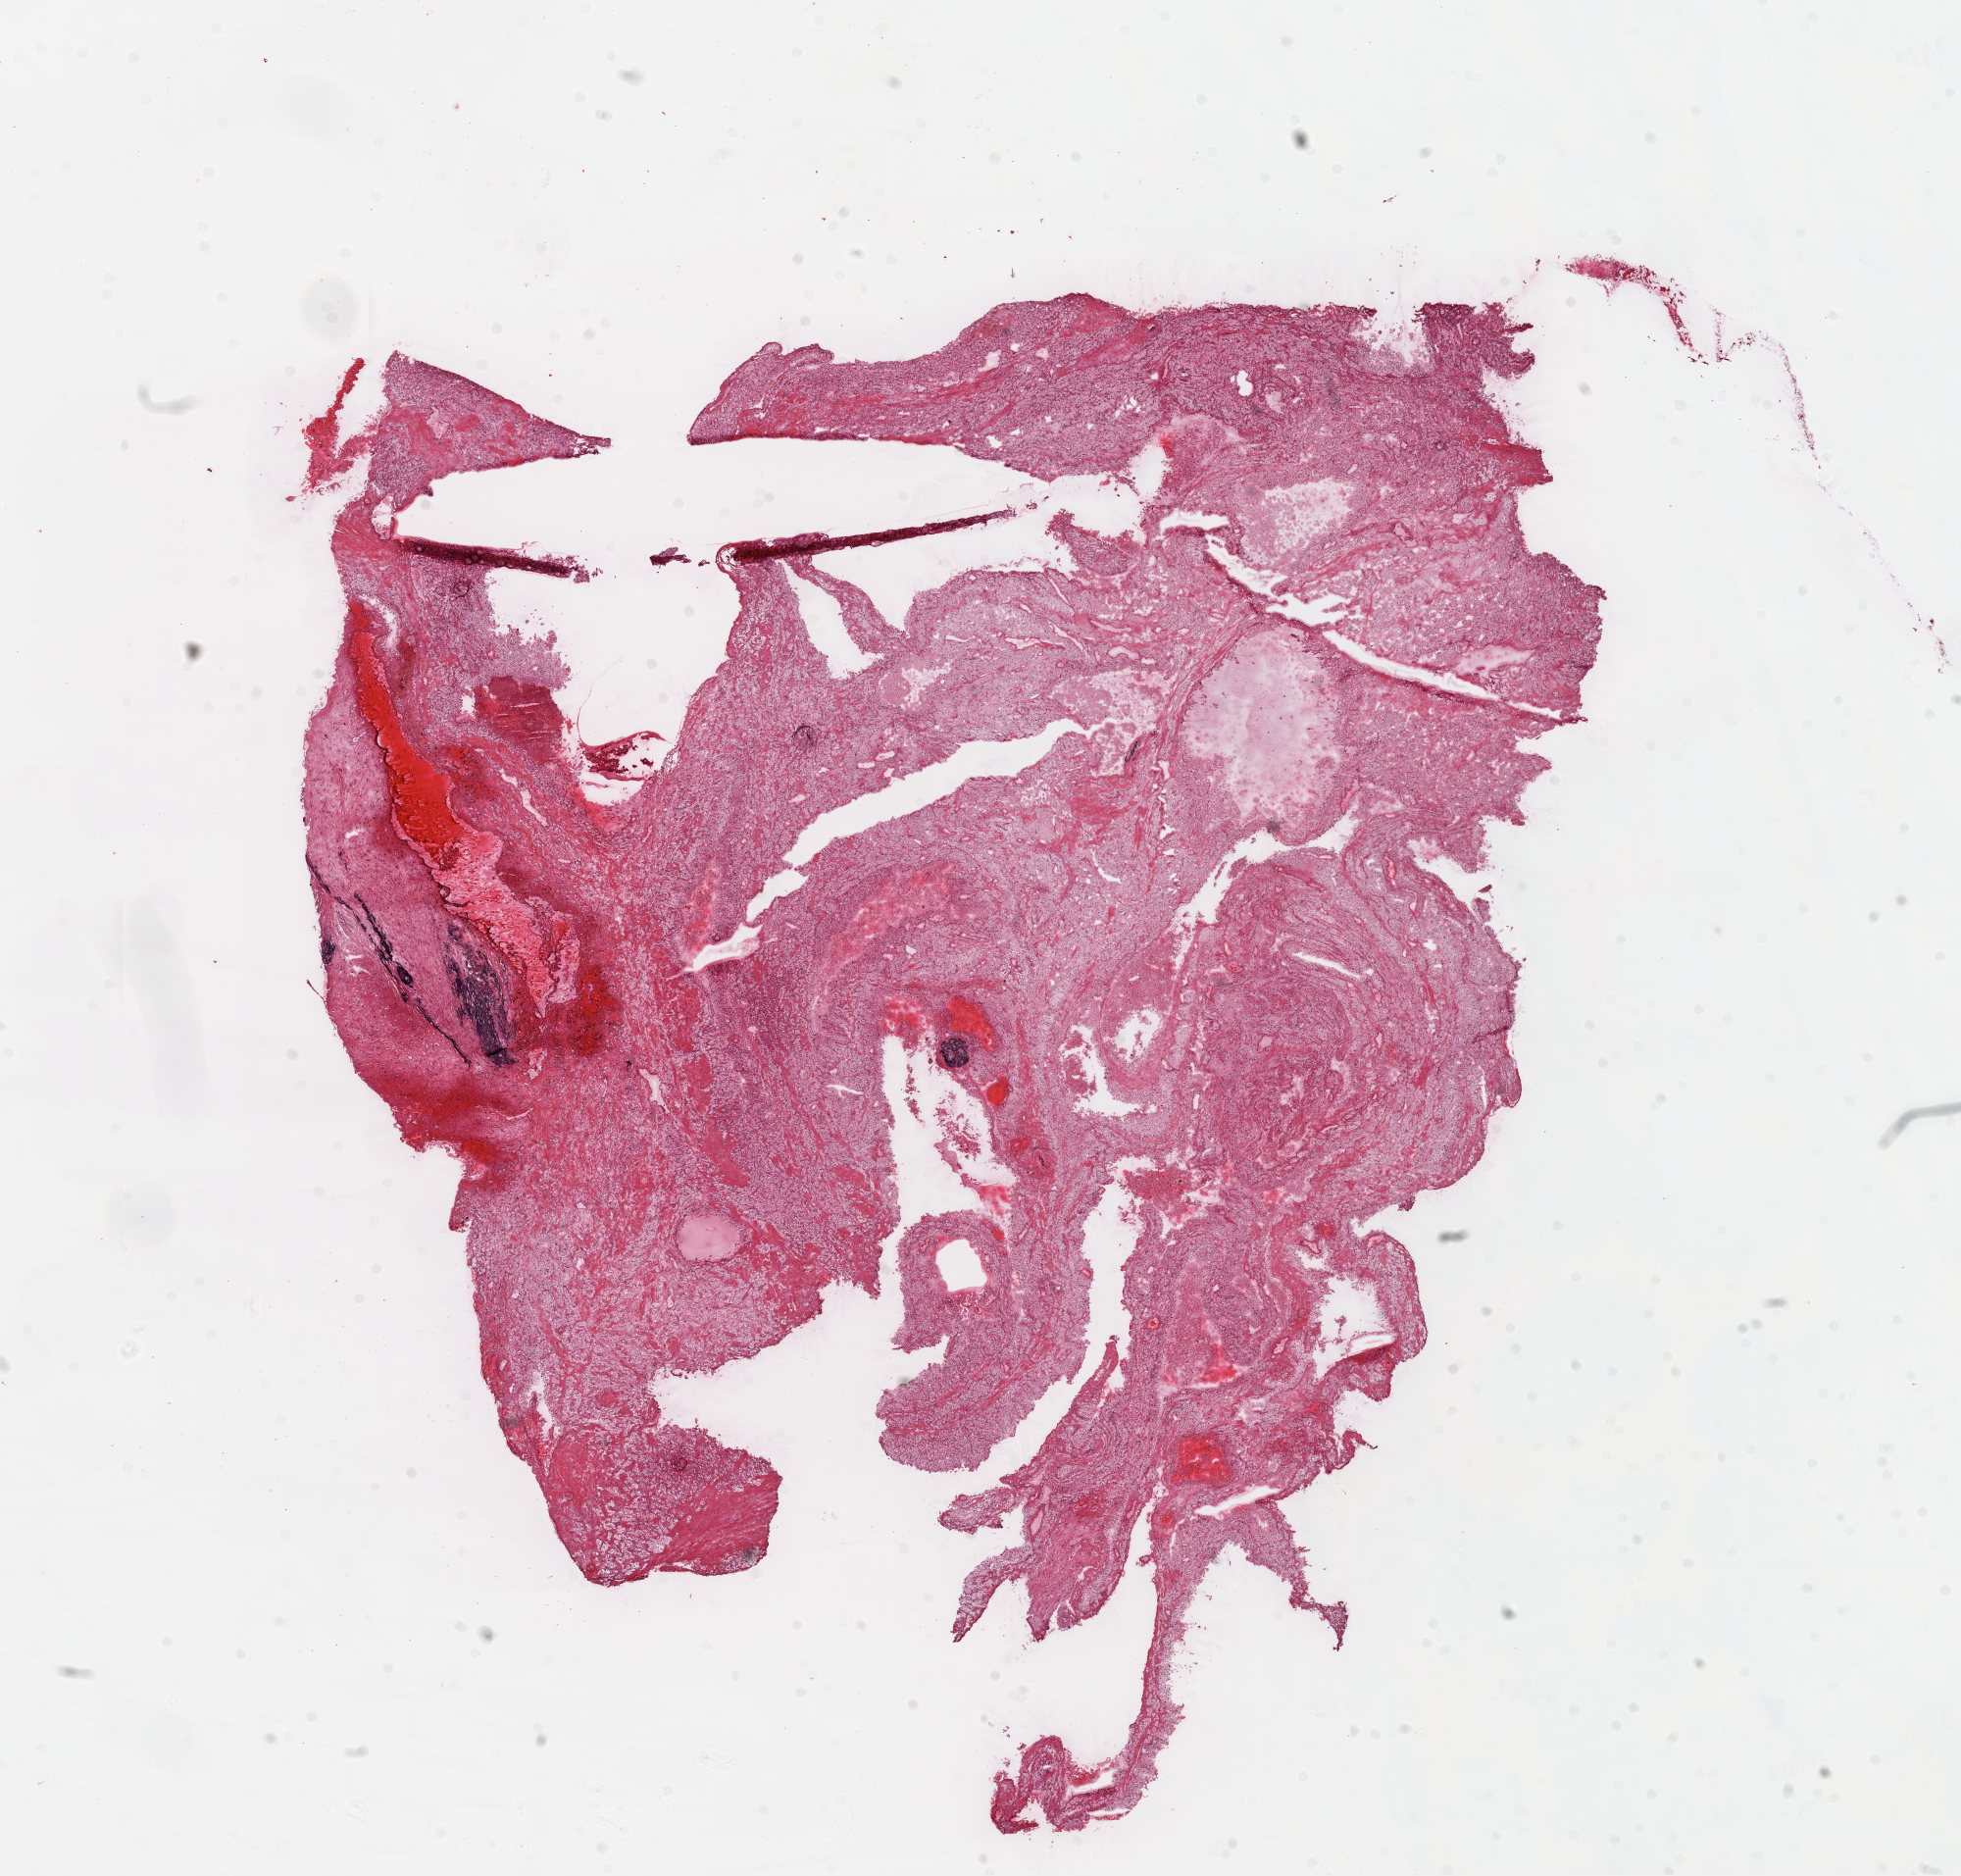
Whole-slide histology image, H&E-stained, shown as a low-resolution overview of the whole scanned area (about 16.0 x 15.4 mm); frozen section; sample: primary tumour, kidney. Female patient; age at initial diagnosis 43 years. Slide review estimates, as recorded: tumour cells 75%, tumour nuclei 80%.
Pathologic diagnosis: Clear cell adenocarcinoma, NOS.